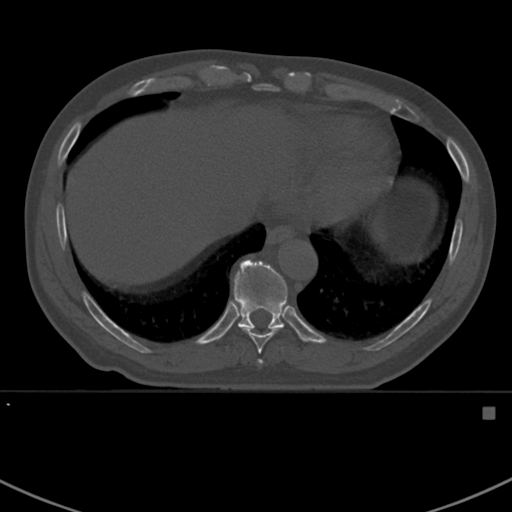
CT including the spine, one axial slice; 120 kVp; bone window (W 1800 / L 400 HU); 512 × 512 image matrix. Male patient, age 59 years. Case-level facts recorded for this patient, not image findings: primary cancer: prostate.
Structures marked on this image (semi-automatic segmentation, software-assisted and operator-edited):
- T10 vertebra: bounding box <234,260,288,330> (left, top, right, bottom; pixels)
- T8 vertebra: <257,359,263,365>
- T9 vertebra: <242,328,282,354>